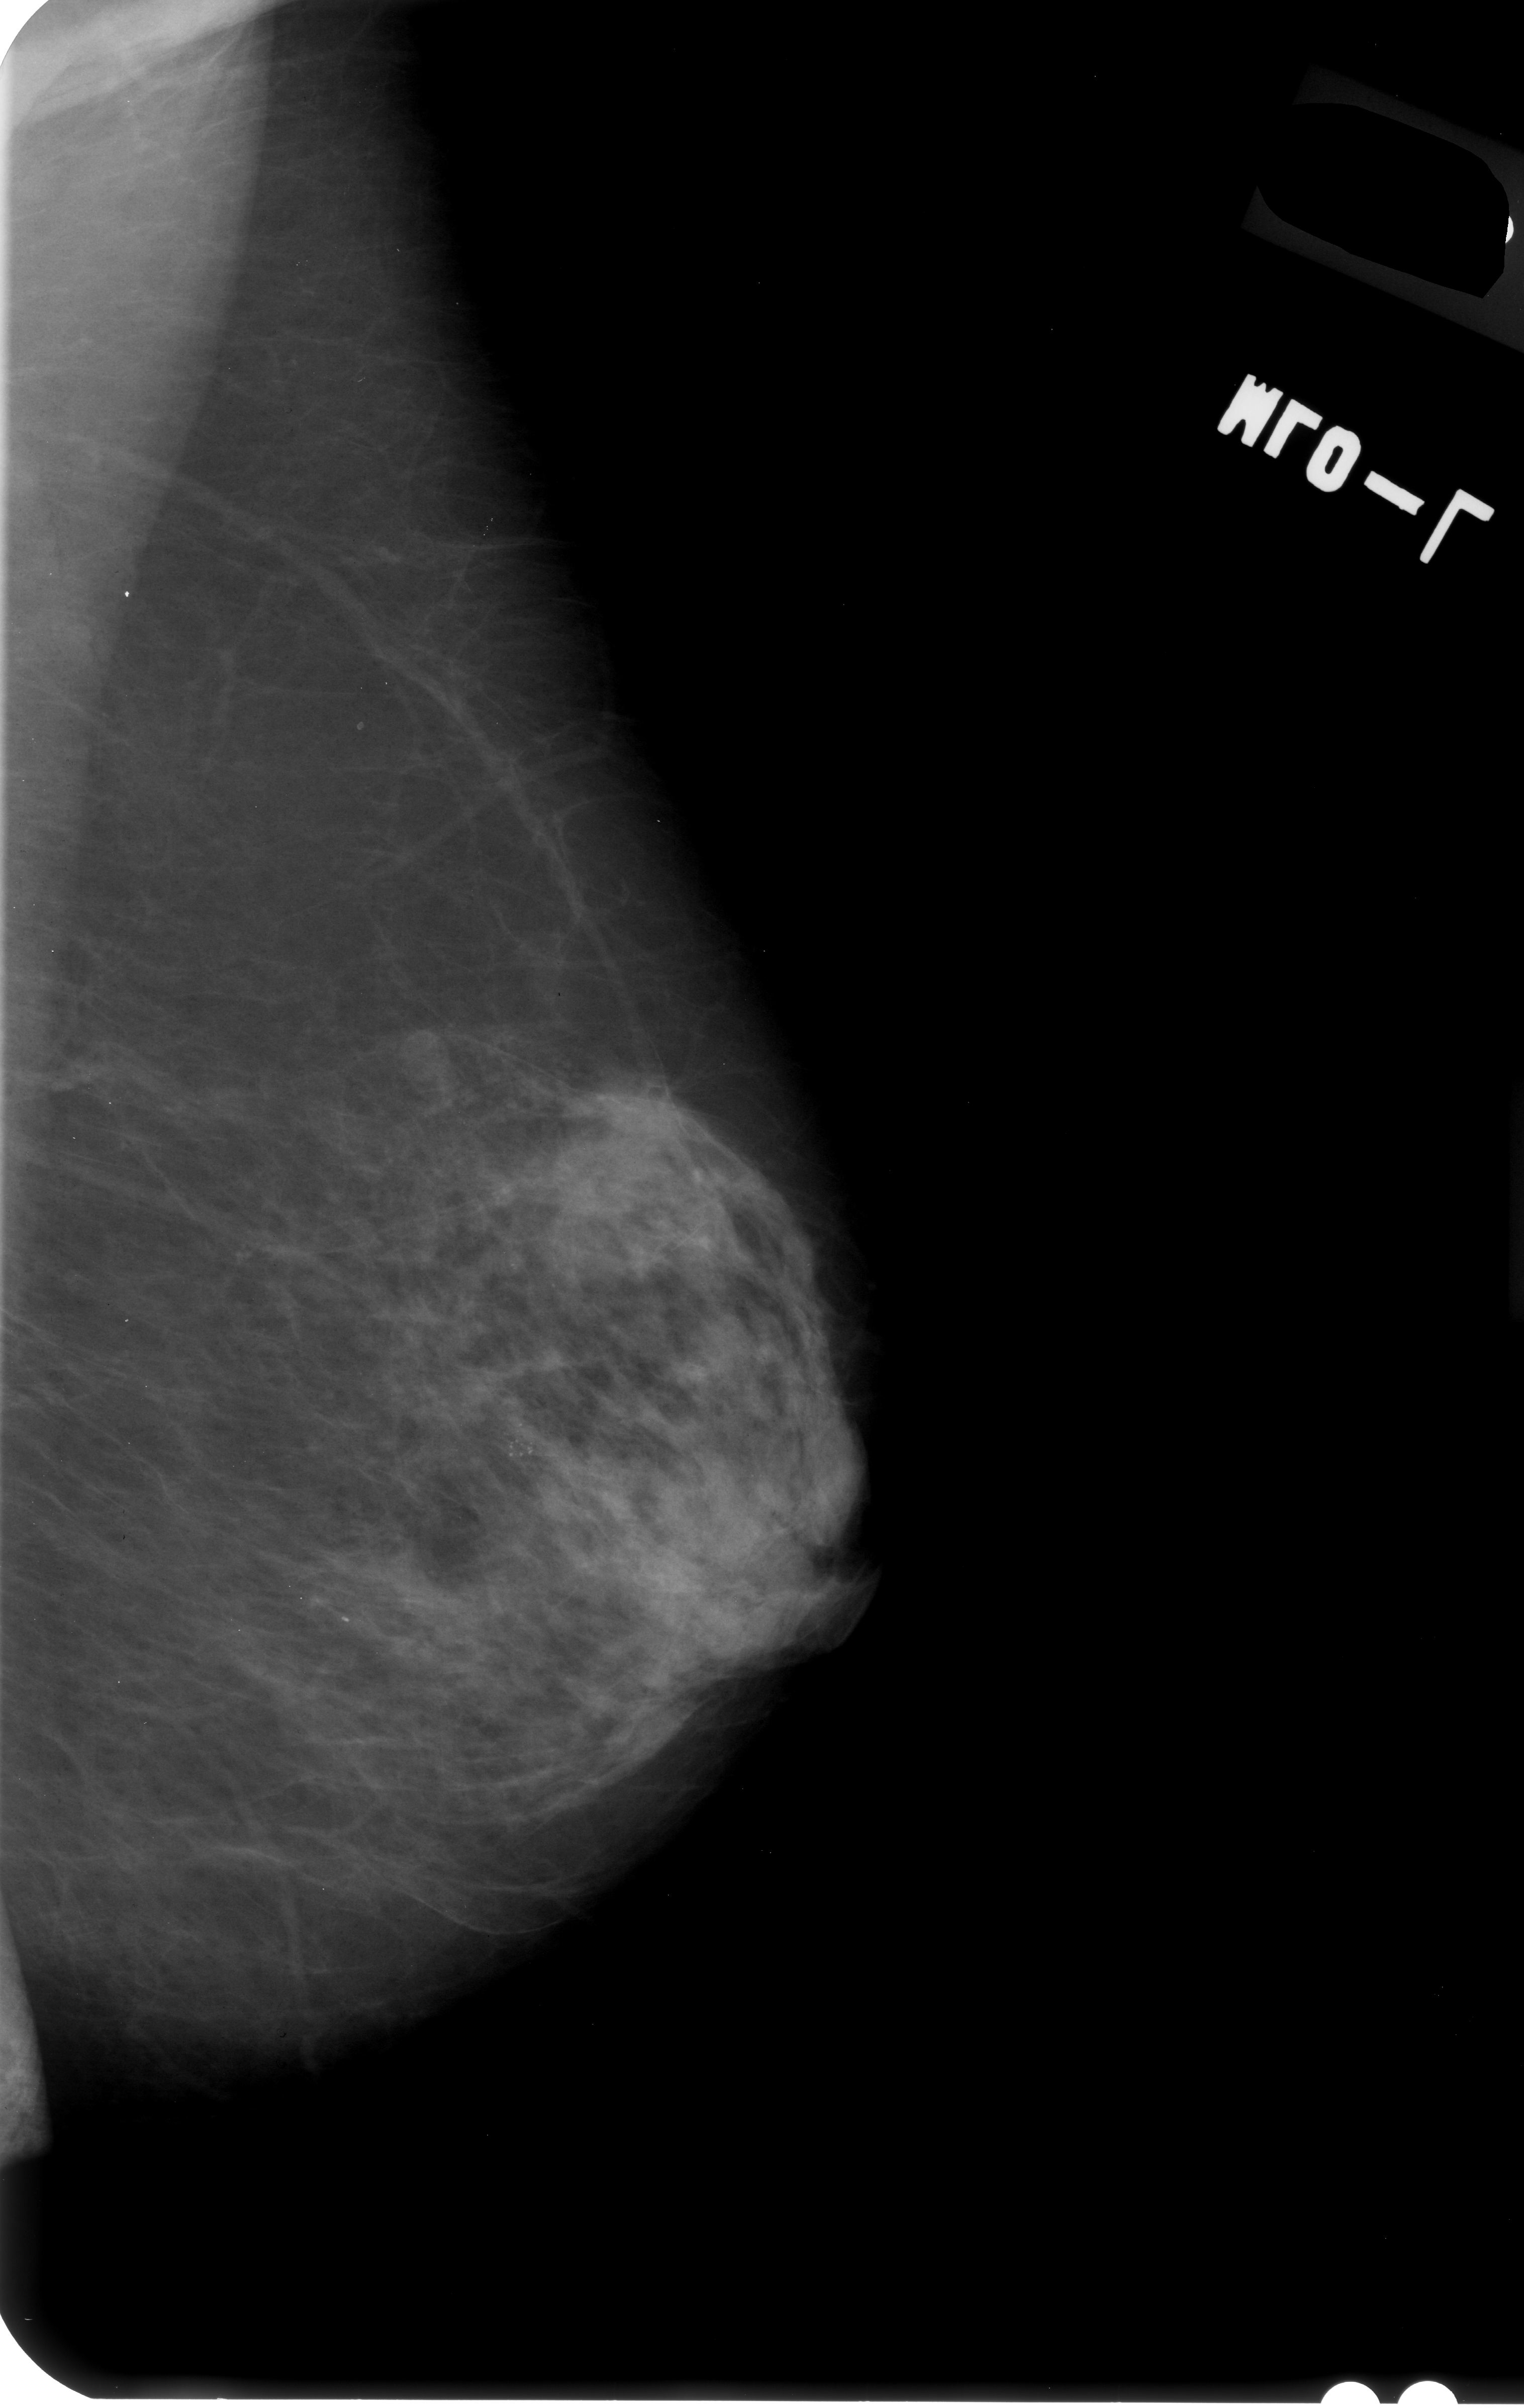
Scanned film-screen mammogram; left breast; mediolateral oblique (MLO) view; BI-RADS breast density category 2 (scale 1–4); 1524 × 2408 image matrix.
Marked abnormalities (boxes around the expert regions of interest):
- calcifications, morphology punctate / pleomorphic, distribution clustered; BI-RADS assessment category 4; pathology result (as recorded, not read from the image): malignant: bounding box (x1, y1, x2, y2) in pixels: (482, 1394, 576, 1496)